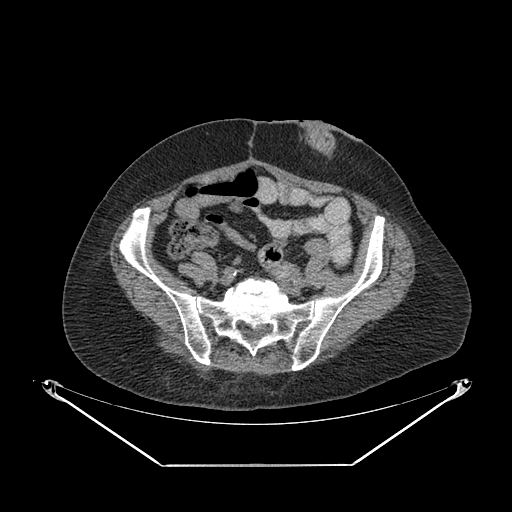
CT of an extremity soft-tissue mass (from a PET/CT study), one axial slice. Slice 78 of 267 in the series (ordered by position). 140 kVp. Soft-tissue window (W 400 / L 40 HU). 512 × 512 image matrix, field of view 500 × 500 mm. Female patient. Case-level facts recorded for this patient, not image findings: histological type: spindle cell suggestive of myxofibrosarcoma; grade: intermediate; site of the primary tumour: right buttock.
Annotated regions visible in this slice (expert contour drawn on MRI and transferred to this co-registered scan by the dataset authors):
- gross tumour volume (mass): box from (x=176, y=352) to (x=245, y=396) px